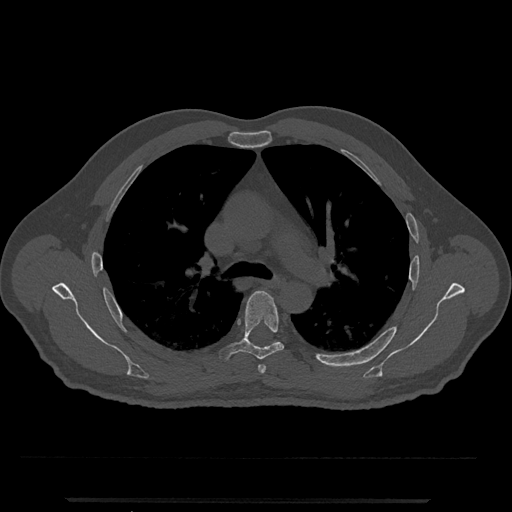
CT including the spine, one axial slice; position 793 of 797 along the scan axis; bone window (W 1800 / L 400 HU); 512 × 512 image matrix. Patient: male, 63 years. Case-level facts recorded for this patient, not image findings: primary cancer: prostate.
Annotated regions visible in this slice (semi-automatic segmentation, software-assisted and operator-edited):
- T5 vertebra: bounding box [x1, y1, x2, y2] px = [219, 291, 284, 361]
- T6 vertebra: [272, 340, 278, 344]